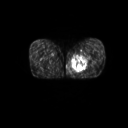
FDG PET of an extremity soft-tissue mass (from a PET/CT study), one axial slice; slice 19 of 267 in the series (ordered by position); 3.27 mm slice thickness; 128 × 128 image matrix. Patient: male, 59 years. From the clinical record (not read from this slice): histological type: pleiomorphic liposarcoma; grade: high; site of the primary tumour: left thigh.
Structures marked on this image (expert contour drawn on MRI and transferred to this co-registered scan by the dataset authors):
- gross tumour volume including surrounding oedema: box from (x=72, y=53) to (x=90, y=73) px
- gross tumour volume (mass): (x=73, y=57)–(x=87, y=72)